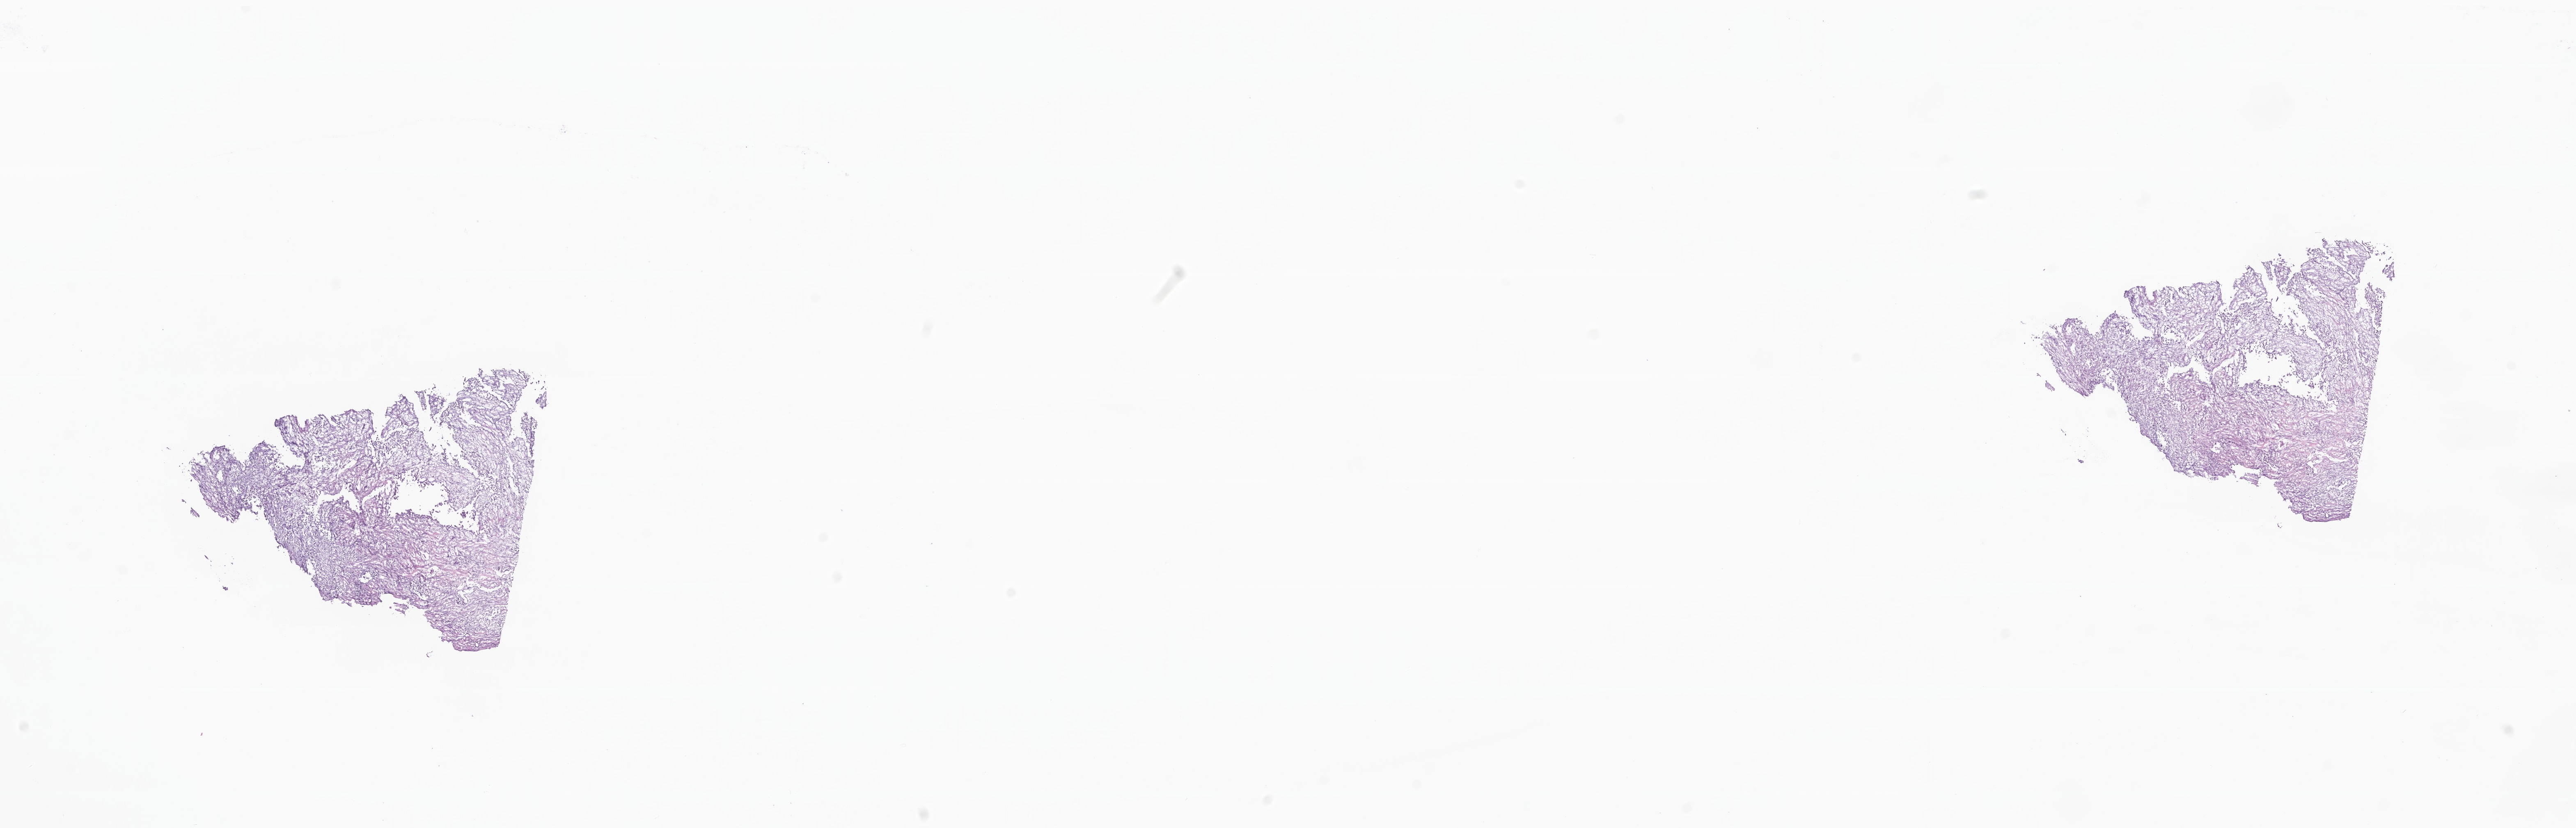
H&E whole-slide image, whole scanned area (about 26.5 x 8.5 mm) shown as a low-resolution overview, cryosection, specimen: primary tumor, anatomic site: tail of pancreas. Patient: male, age at initial diagnosis 64 years. Slide review estimates, as recorded: tumor cells 50%, tumor nuclei 60%, stromal cells 50%, necrosis 0%, normal cells 0%. Infiltration values recorded for this section: lymphocyte infiltration 0%, monocyte infiltration 0%, neutrophil infiltration 0%.
* diagnosis: Mixed adenoneuroendocrine carcinoma